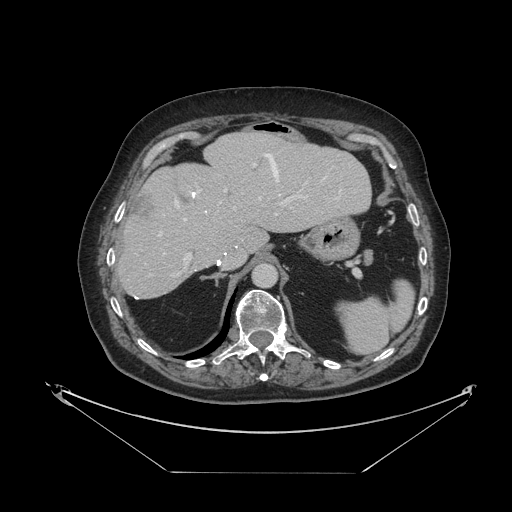
Contrast-enhanced abdominal CT, one axial slice. Slice 73 of 121 in the series (ordered by position). Reconstruction kernel STANDARD. Intravenous contrast given. Soft-tissue window (W 400 / L 40 HU). 512 × 512 image matrix, field of view 500 × 500 mm. Male patient, age 68 years. From the clinical record (not read from this slice): diagnosis: colorectal cancer liver metastases, imaged before liver resection; multiple liver metastases: no; largest metastasis: 4 cm.
Annotated regions visible in this slice (manually delineated by an expert):
- hepatic veins: bounding box (x1, y1, x2, y2) in pixels: (159, 154, 325, 236)
- liver: (119, 133, 371, 299)
- planned liver remnant (the part of the liver to remain after resection): (118, 133, 371, 299)
- portal vein (with intrahepatic branches): (172, 164, 302, 277)
- liver metastasis: (132, 191, 156, 220)